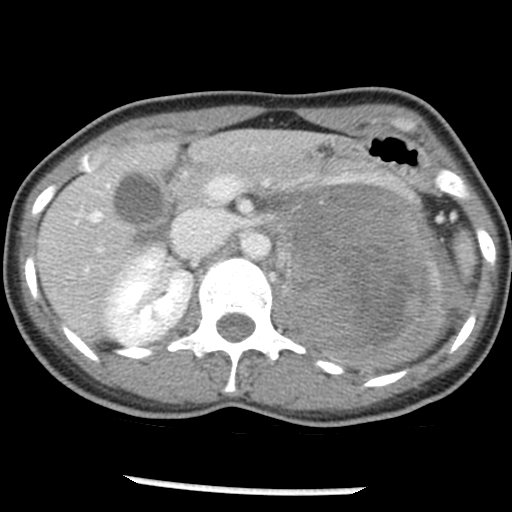
Contrast-enhanced abdominal CT, one axial slice. Position 28 of 54 along the scan axis. 120 kVp. Intravenous contrast given. Soft-tissue window (W 400 / L 40 HU). 5 mm slice thickness. 512 × 512 image matrix, field of view 240 × 240 mm. Patient: female, 33 years. From the clinical record (not read from this slice): diagnosis: adrenocortical carcinoma; tumour side: left adrenal; tumour size at pathology: 11 cm; Ki-67 index: 20 %; stage (as recorded): 2.
Structures marked on this image (semi-automatic segmentation, software-assisted and operator-edited):
- mass: bounding box <278,185,457,365> (left, top, right, bottom; pixels)